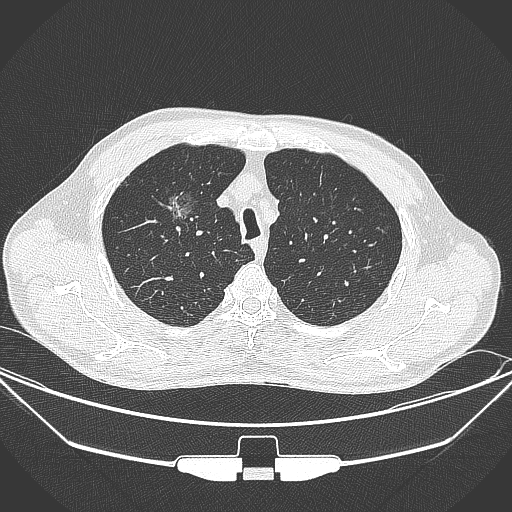
Chest CT, one axial slice. Position 274 of 355 along the scan axis. Lung window (W 1500 / L -600 HU). 512 × 512 image matrix. Patient: male, 67 years. From the clinical record (not read from this slice): clinical TNM (as recorded): T1c N0 M0; histopathological grade: G2.
Annotated regions visible in this slice (bounding box drawn by a radiologist):
- lung tumour (recorded histology: adenocarcinoma): bounding box <159,187,206,233> (left, top, right, bottom; pixels)